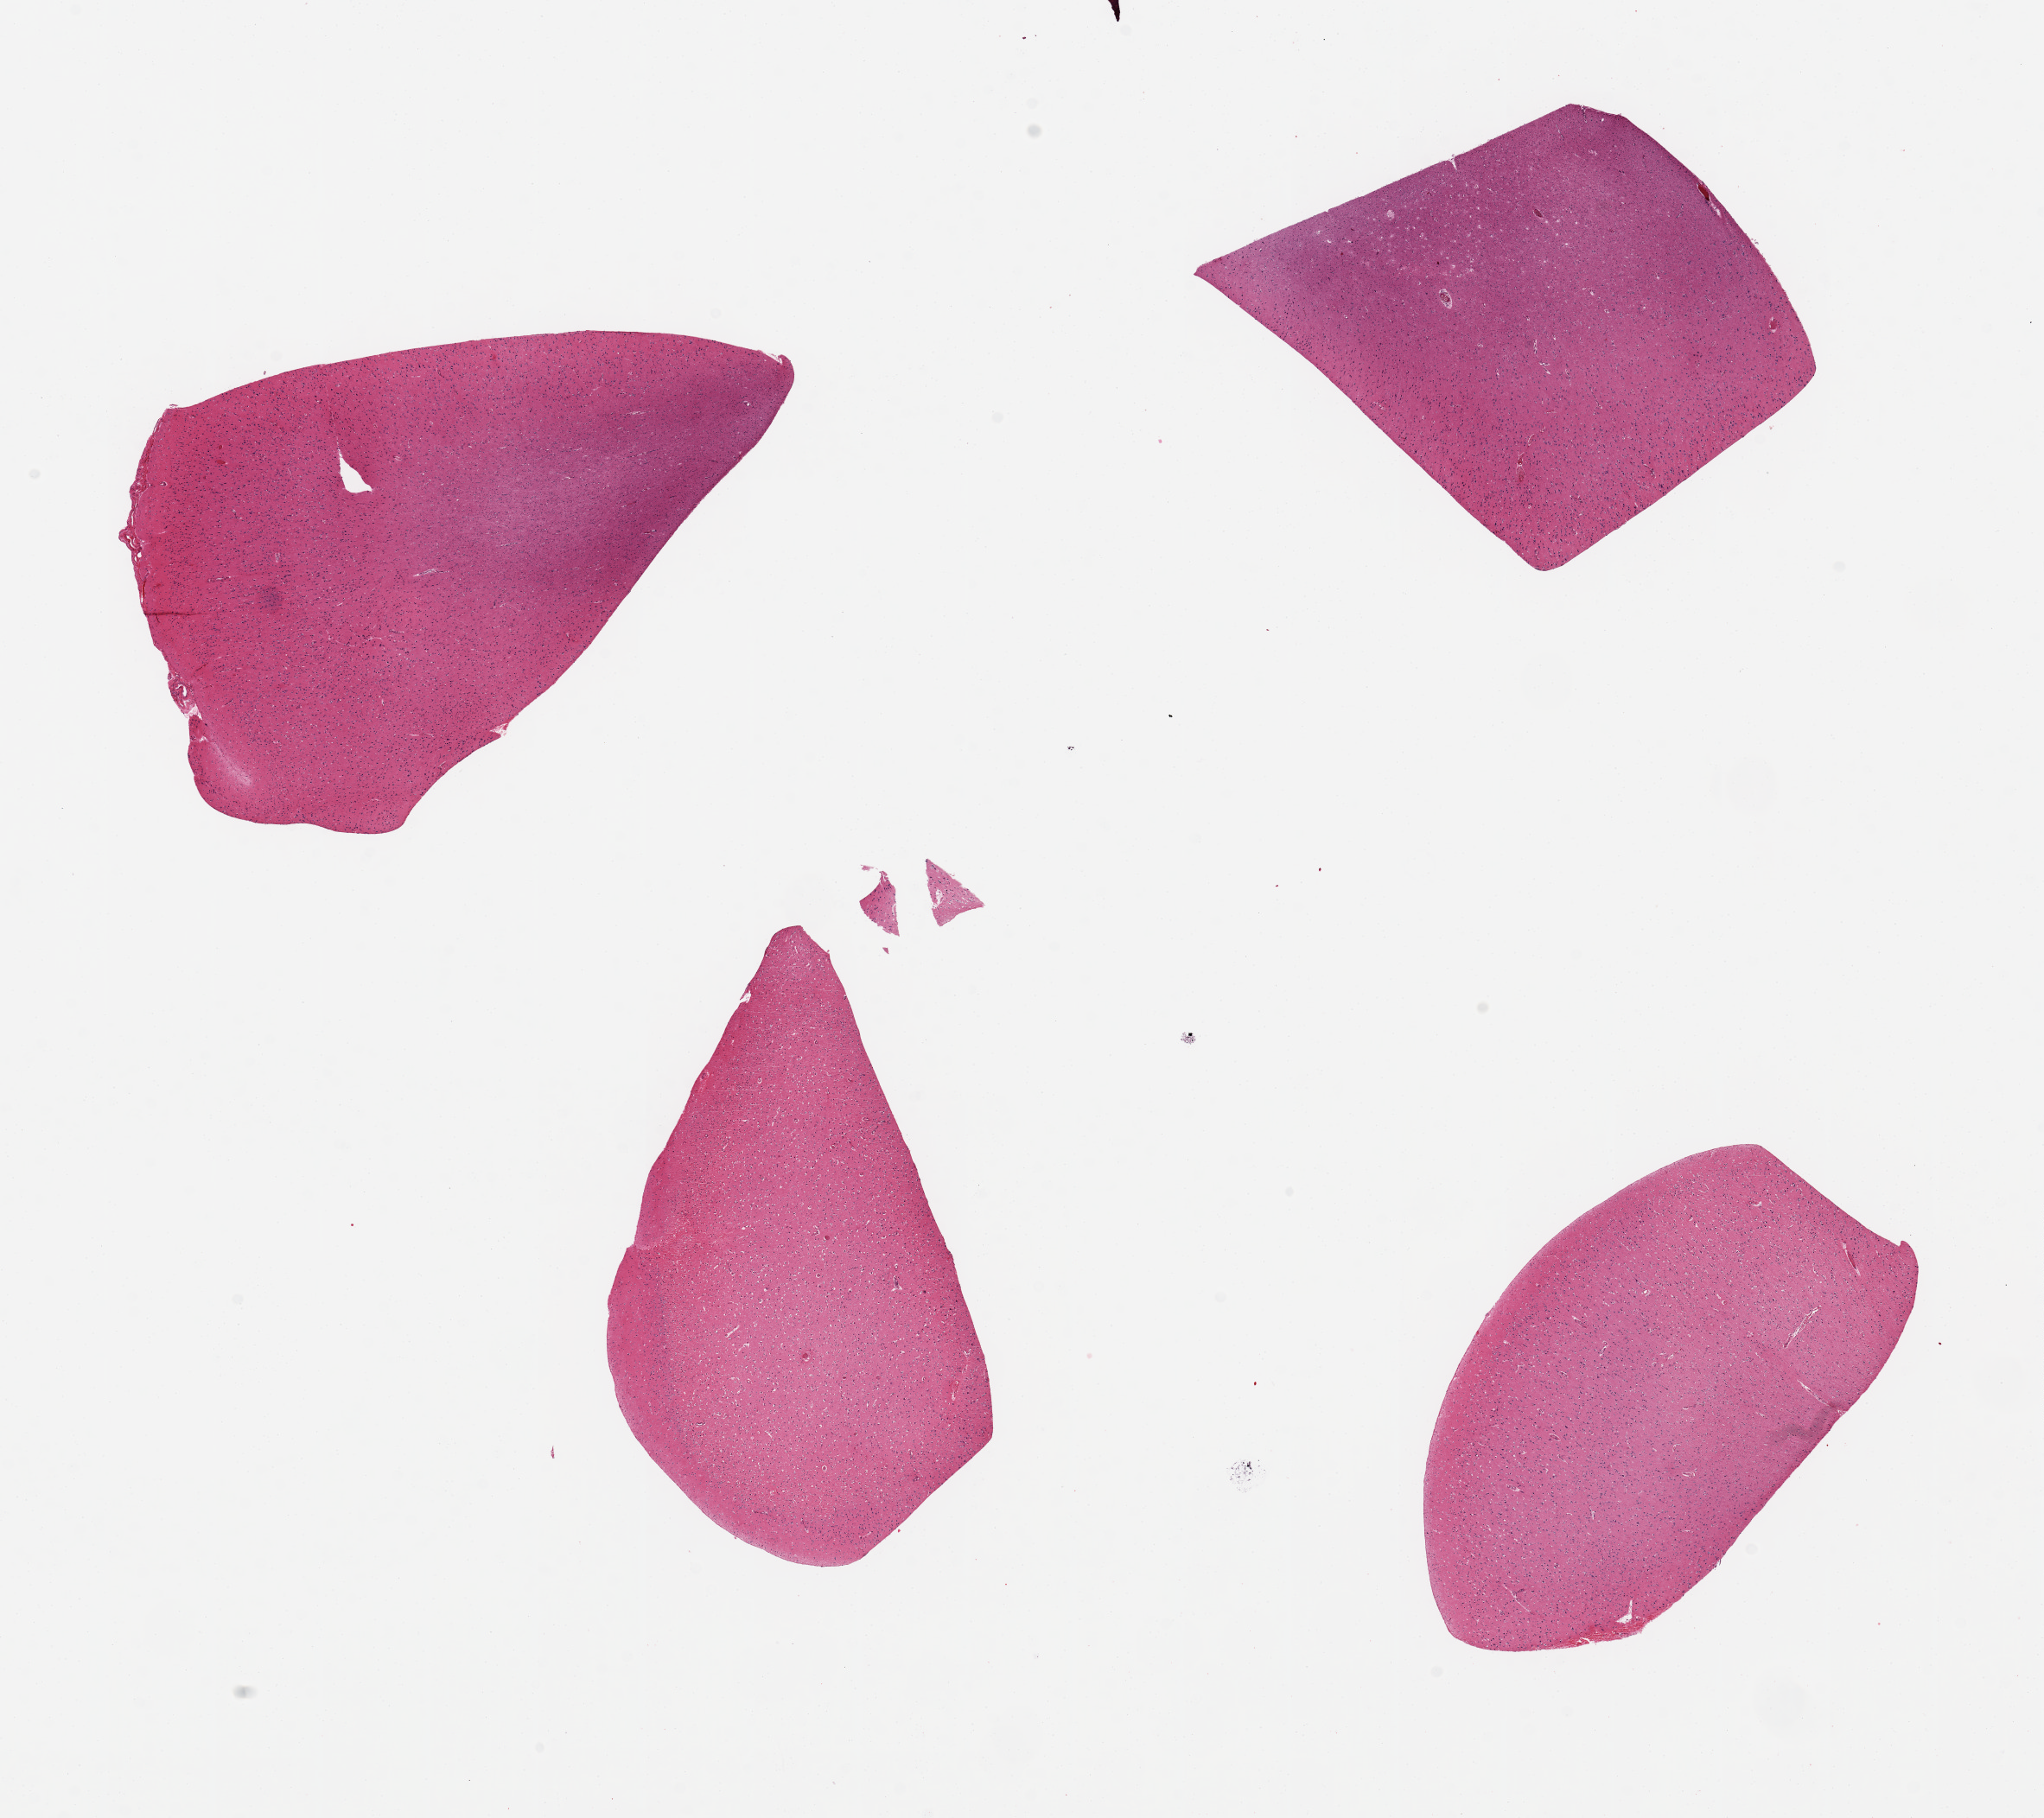
Digitized H&E-stained section, whole scanned area (about 18.7 x 16.6 mm, slide scanned at 20x) shown as a low-resolution overview; PAXgene-fixed paraffin-embedded (PFPE) section; target tissue: cerebral cortex; tissue donor sample. Male donor.
* pathologist's review note for this sample: 4 pieces ~5x3 mm